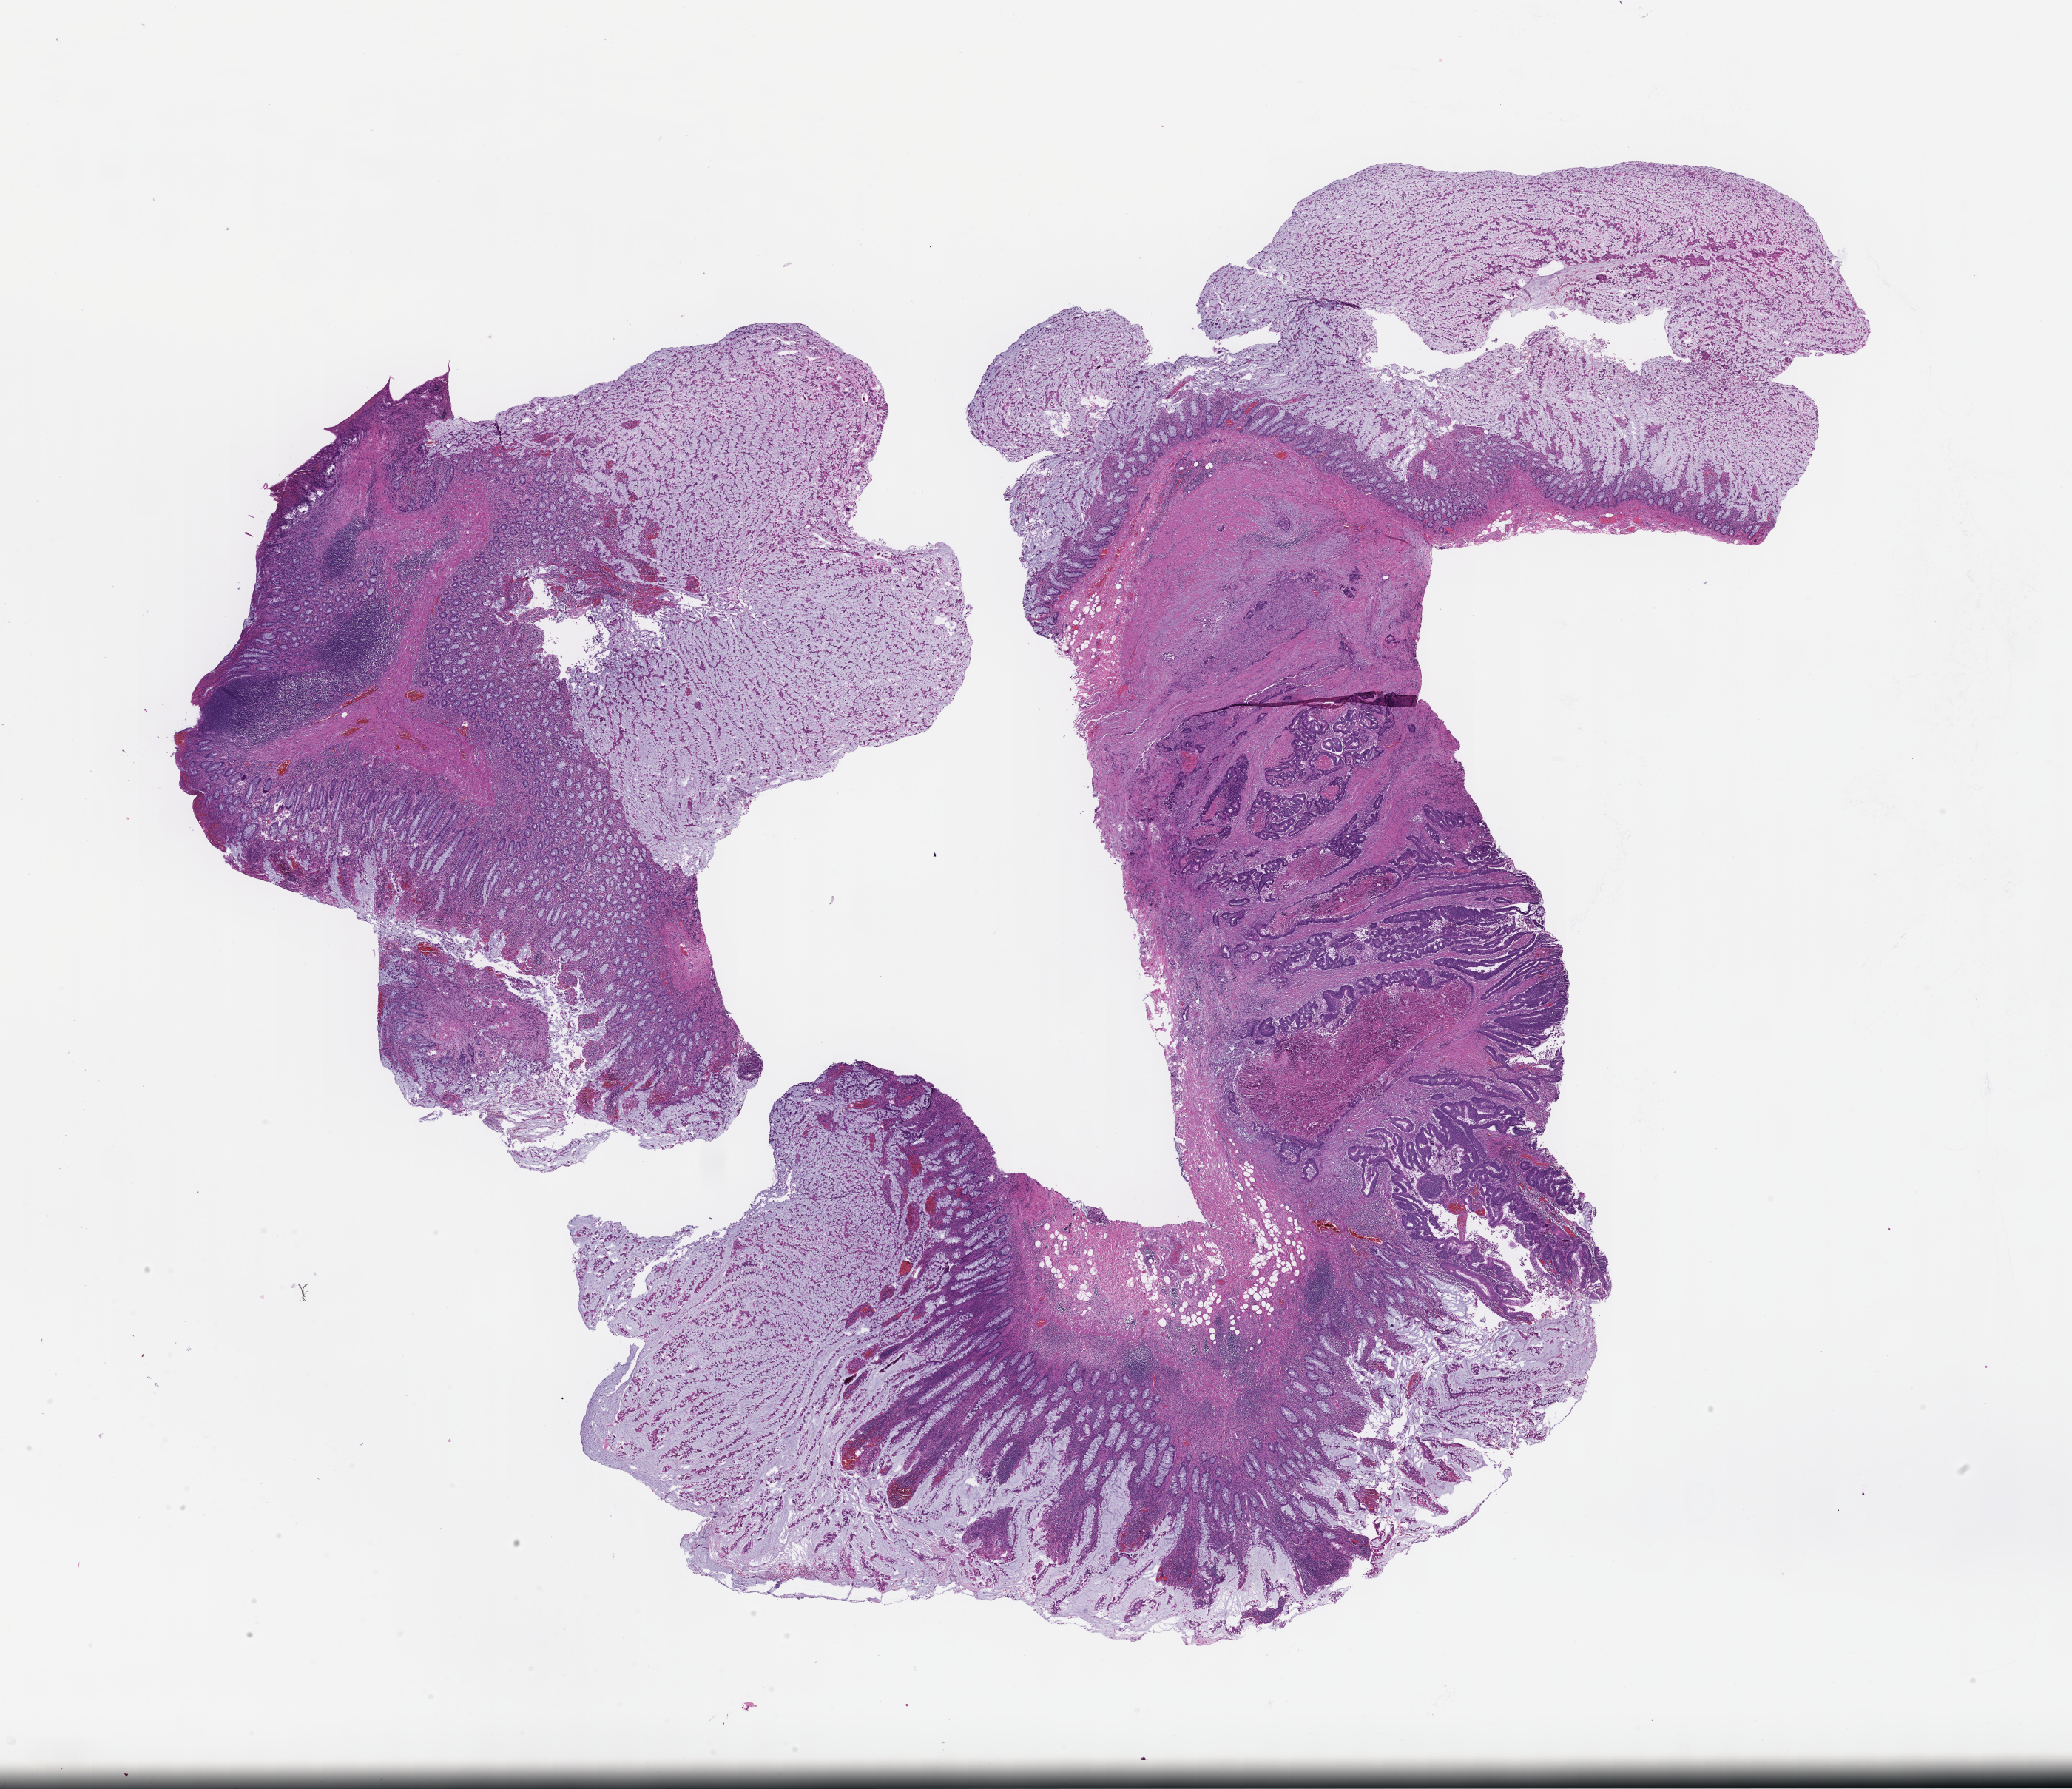
Whole-slide image, hematoxylin and eosin (H&E) stain — whole scanned area (about 22.6 x 19.5 mm) shown as a low-resolution overview. Formalin-fixed, paraffin-embedded (FFPE) tissue. Tissue site: colon. Patient: male.
This section: primary tumour tissue. Diagnosis: Colorectal Carcinoma.